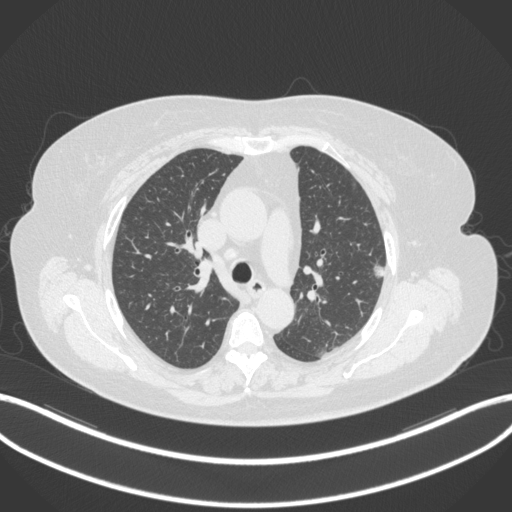
Chest CT, one axial slice; slice 217 of 310 in the series (ordered by position); 120 kVp; lung window (W 1500 / L -600 HU); 1 mm slice thickness; 512 × 512 image matrix, field of view 400 × 400 mm. Female patient, age 70 years. Case-level facts recorded for this patient, not image findings: clinical TNM (as recorded): T1c N0 M0.
Structures marked on this image (bounding box drawn by a radiologist):
- lung tumour (recorded histology: adenocarcinoma): bounding box <373,263,386,280> (left, top, right, bottom; pixels)